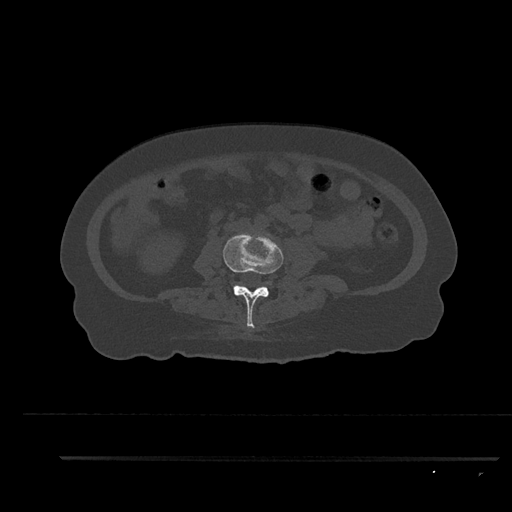
CT including the spine, one axial slice. Slice 71 of 797 in the series (ordered by position). Reconstruction kernel Br40s/3. Bone window (W 1800 / L 400 HU). 0.5 mm slice thickness. 512 × 512 image matrix, field of view 408 × 408 mm. Female patient, age 44 years. Case-level facts recorded for this patient, not image findings: primary cancer: renal.
Structures marked on this image (semi-automatic segmentation, software-assisted and operator-edited):
- L3 vertebra: bounding box (x1, y1, x2, y2) in pixels: (223, 232, 284, 329)